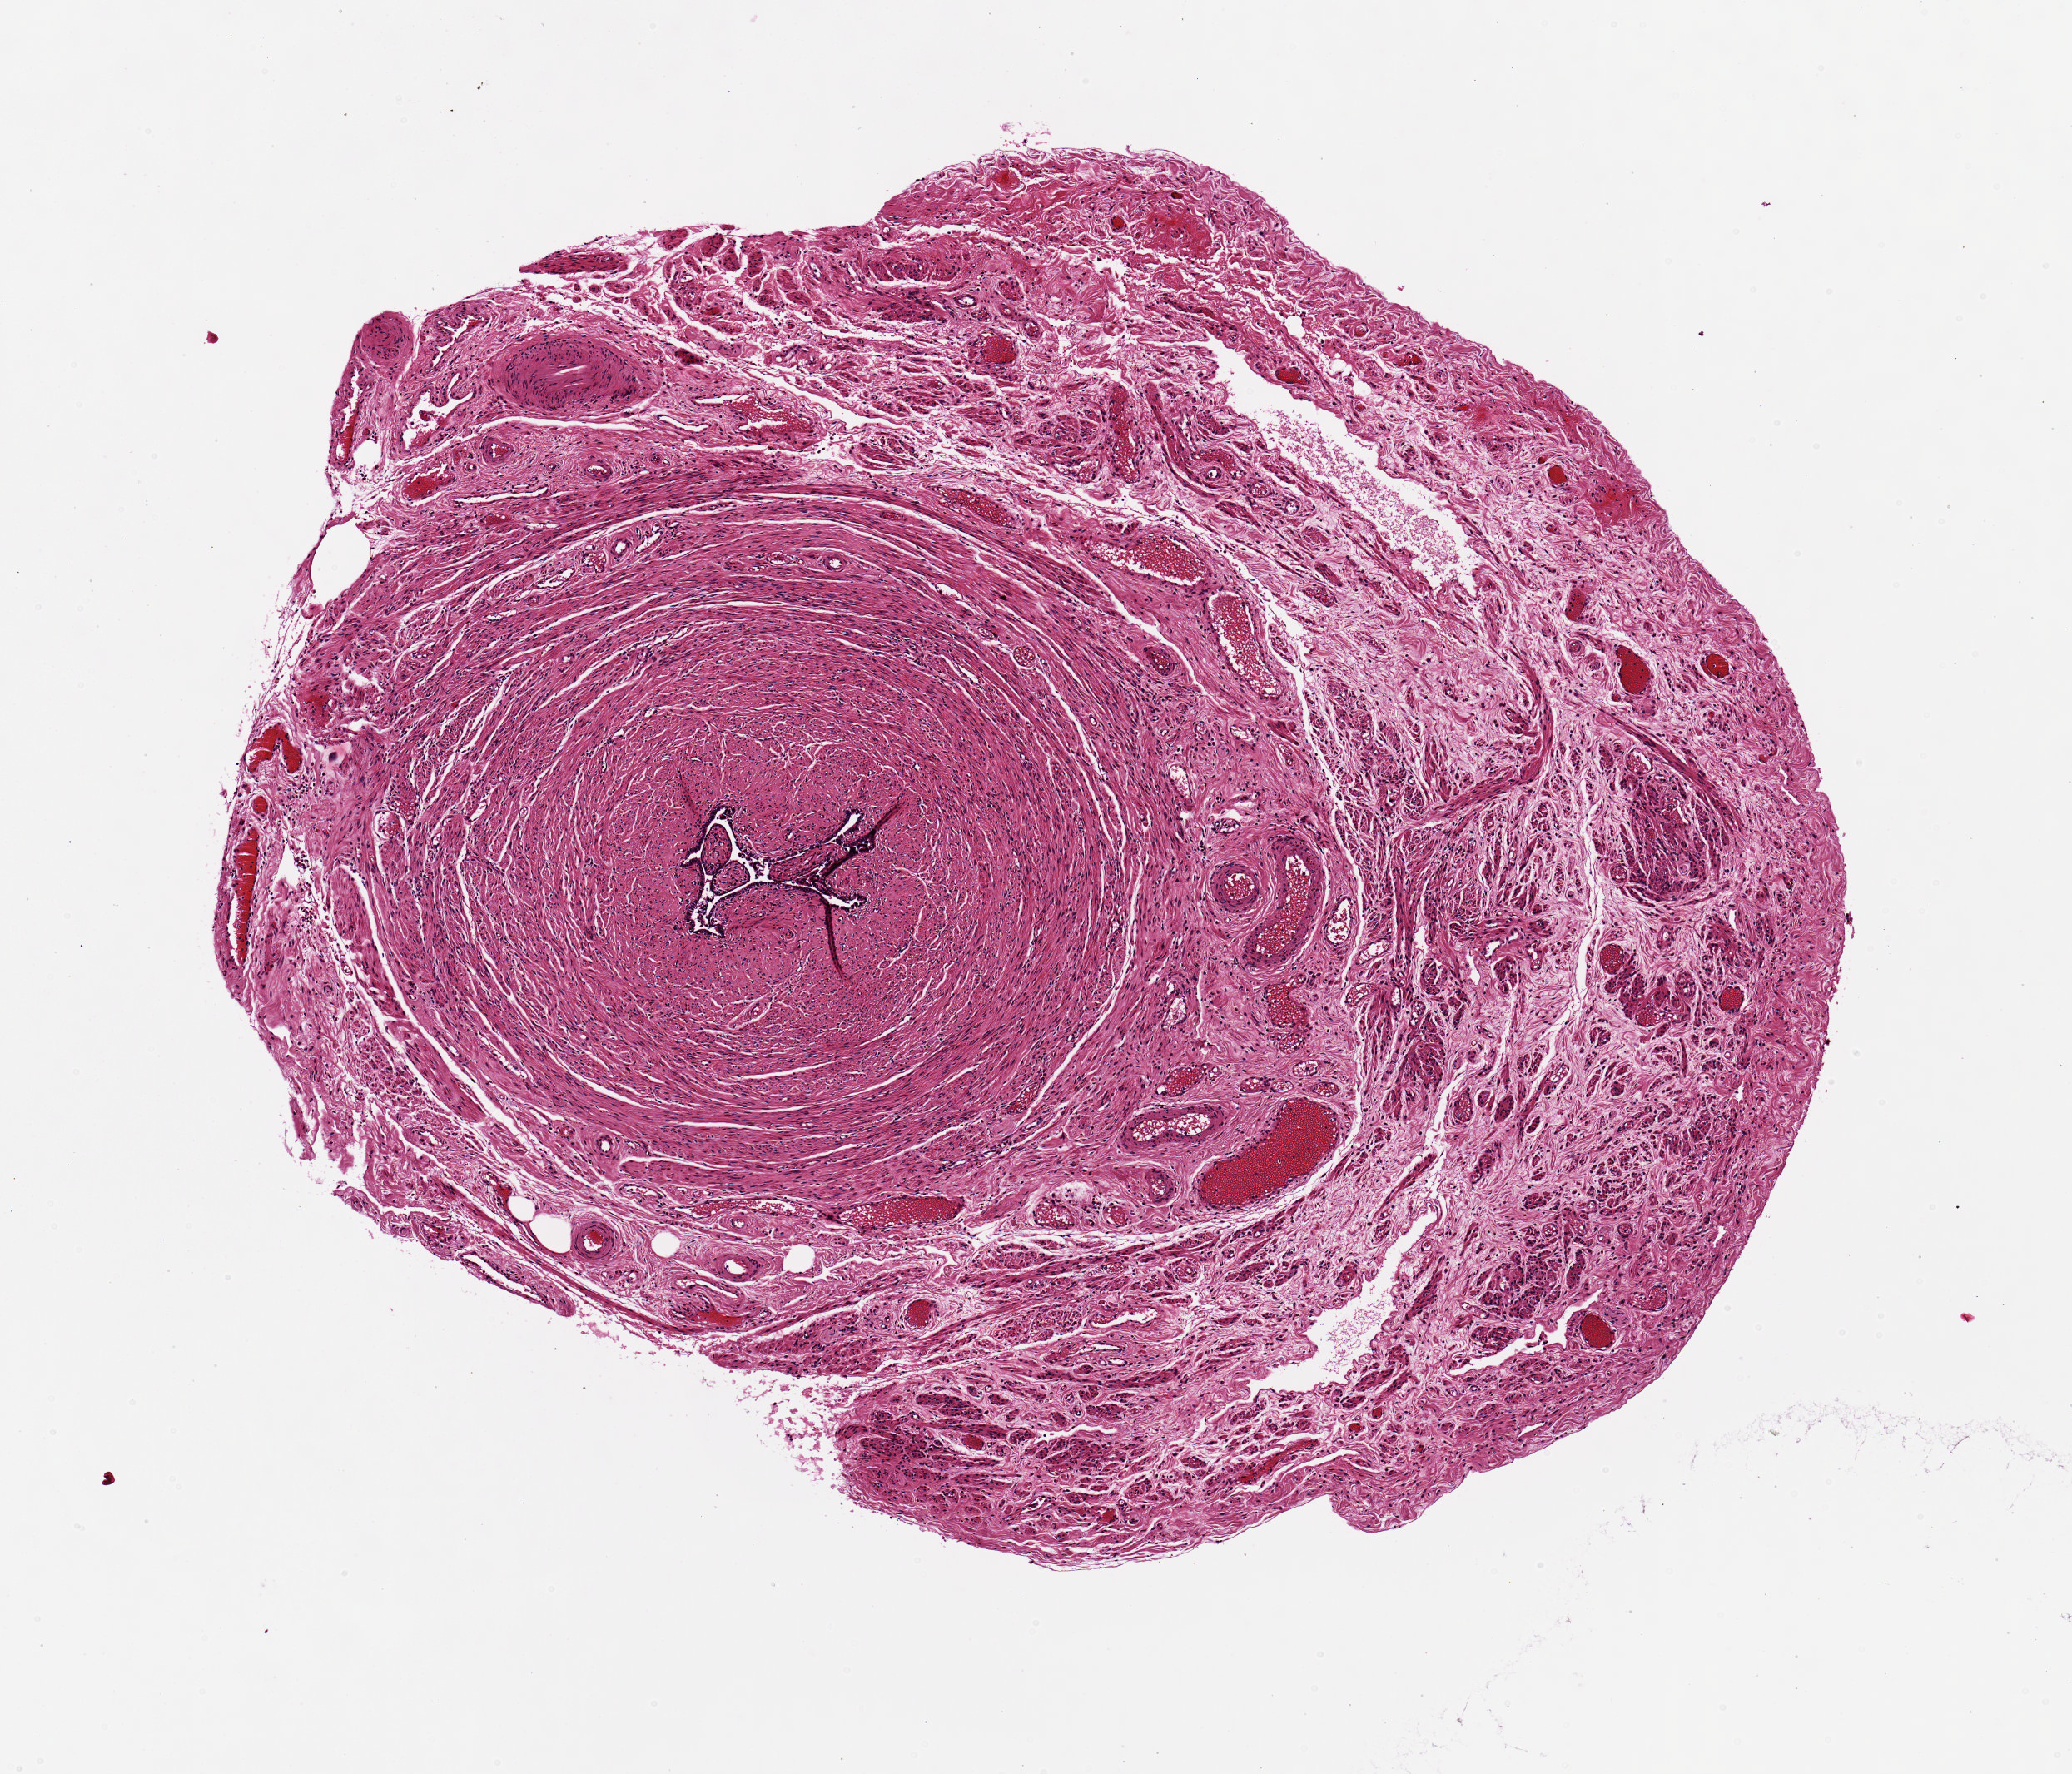
Whole-slide image, haematoxylin and eosin stain, low-resolution overview of the scanned area, about 4.9 x 4.2 mm, PAXgene-fixed paraffin-embedded (PFPE) section, section of fallopian tube (target tissue), donor tissue sample. Female donor.
* pathologist's review note for this sample: lumen is ~0.4 x0.4mm; overall section is 3.5x3.5mm